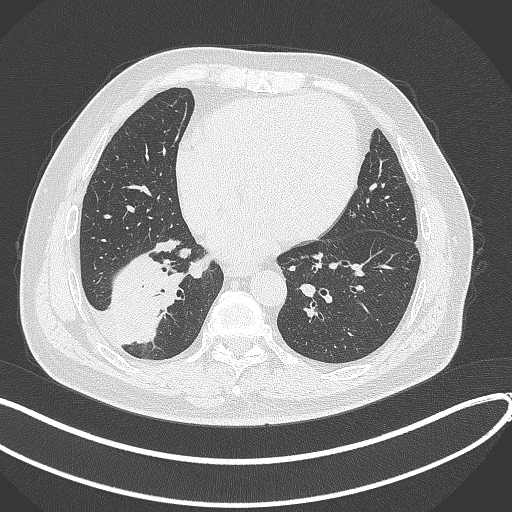
Chest CT, one axial slice; 120 kVp; lung window (W 1500 / L -600 HU); 1 mm slice thickness; 512 × 512 image matrix, field of view 400 × 400 mm. Patient: male, 59 years.
Structures marked on this image (rectangle marked by the reading radiologist):
- lung tumour (recorded histology: adenocarcinoma): bounding box (x1, y1, x2, y2) in pixels: (112, 247, 187, 349)